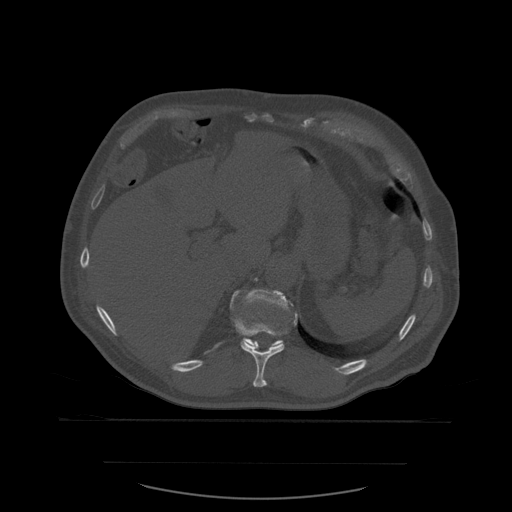
CT including the spine, one axial slice. Position 289 of 590 along the scan axis. Bone window (W 1800 / L 400 HU). 1.25 mm slice thickness. 512 × 512 image matrix, field of view 479 × 479 mm. Patient age 71 years. Case-level facts recorded for this patient, not image findings: primary cancer: lung.
Structures marked on this image (semi-automatic segmentation, software-assisted and operator-edited):
- T11 vertebra: box from (x=235, y=312) to (x=298, y=387) px
- T12 vertebra: (x=230, y=289)–(x=298, y=346)